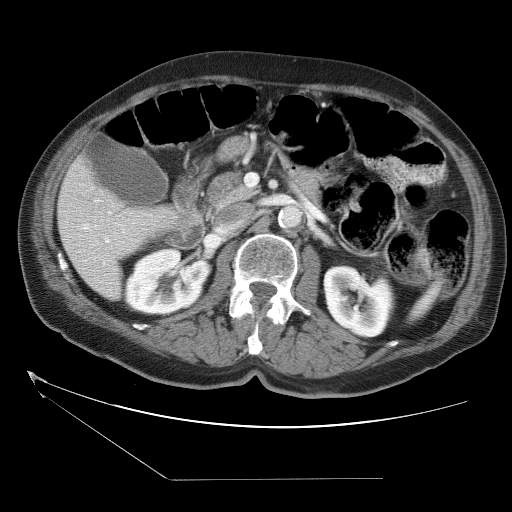
Contrast-enhanced abdominal CT (liver protocol), one axial slice; position 12 of 38 along the scan axis; reconstruction kernel STANDARD; 120 kVp; one of 2 acquisitions stored at this slice position; soft-tissue window (W 400 / L 40 HU); 5 mm slice thickness; 512 × 512 image matrix. From the clinical record (not read from this slice): diagnosis: hepatocellular carcinoma (patient treated with transarterial chemoembolisation; whether this scan precedes or follows treatment is not stated here); TNM stage (as recorded): Stage-II; Child-Pugh class: A.
Structures marked on this image (semi-automatically segmented with operator editing):
- liver parenchyma outside the tumour (the mass and vessels are separate outlines, so this box may not span the whole liver): bounding box [x1, y1, x2, y2] px = [58, 154, 178, 298]
- liver vessels: [82, 223, 124, 243]